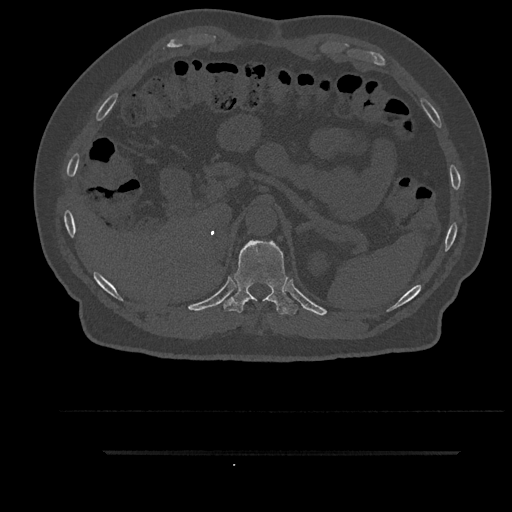
CT including the spine, one axial slice. Slice 315 of 797 in the series (ordered by position). Reconstruction kernel Br40s/3. 120 kVp. Bone window (W 1800 / L 400 HU). 0.5 mm slice thickness. 512 × 512 image matrix, field of view 432 × 432 mm. Patient: male, 63 years. From the clinical record (not read from this slice): primary cancer: renal; vertebrae with lytic lesions (as recorded): T8.
Outlined on this slice (semi-automatically segmented with operator editing):
- T11 vertebra: bounding box <224,240,298,316> (left, top, right, bottom; pixels)